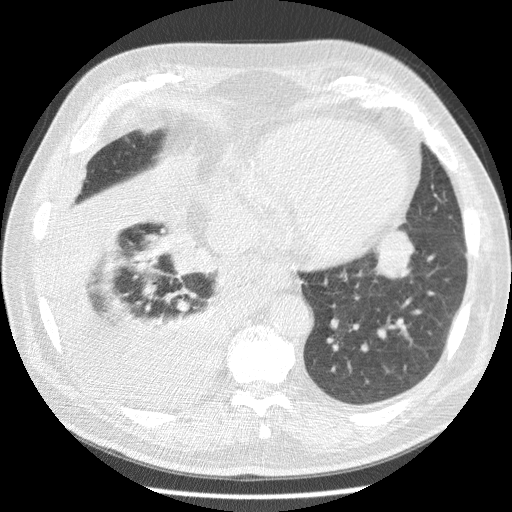
Axial slice from a low-dose chest CT screening exam; third annual screen; lung window (W 1500 / L -600 HU); 2.5 mm slice thickness. Male participant, aged 63 years at enrolment. Current smoker at enrolment.
Lesion marked by an expert reader, bounding box <350,224,417,295> (left, top, right, bottom; pixels). The exam's reader record, not a measurement of the box and not confirmed to be the same lesion: non-calcified nodule or mass ≥4 mm, left lower lobe, 34 × 31 mm, smooth margins, soft tissue attenuation, pre-existing on the prior screen: yes; interval growth: yes. Participant outcome: lung cancer diagnosed 30 days after this screen — squamous cell carcinoma, NOS, left lower lobe, stage IB (AJCC 6th edition), 48 mm at pathology.